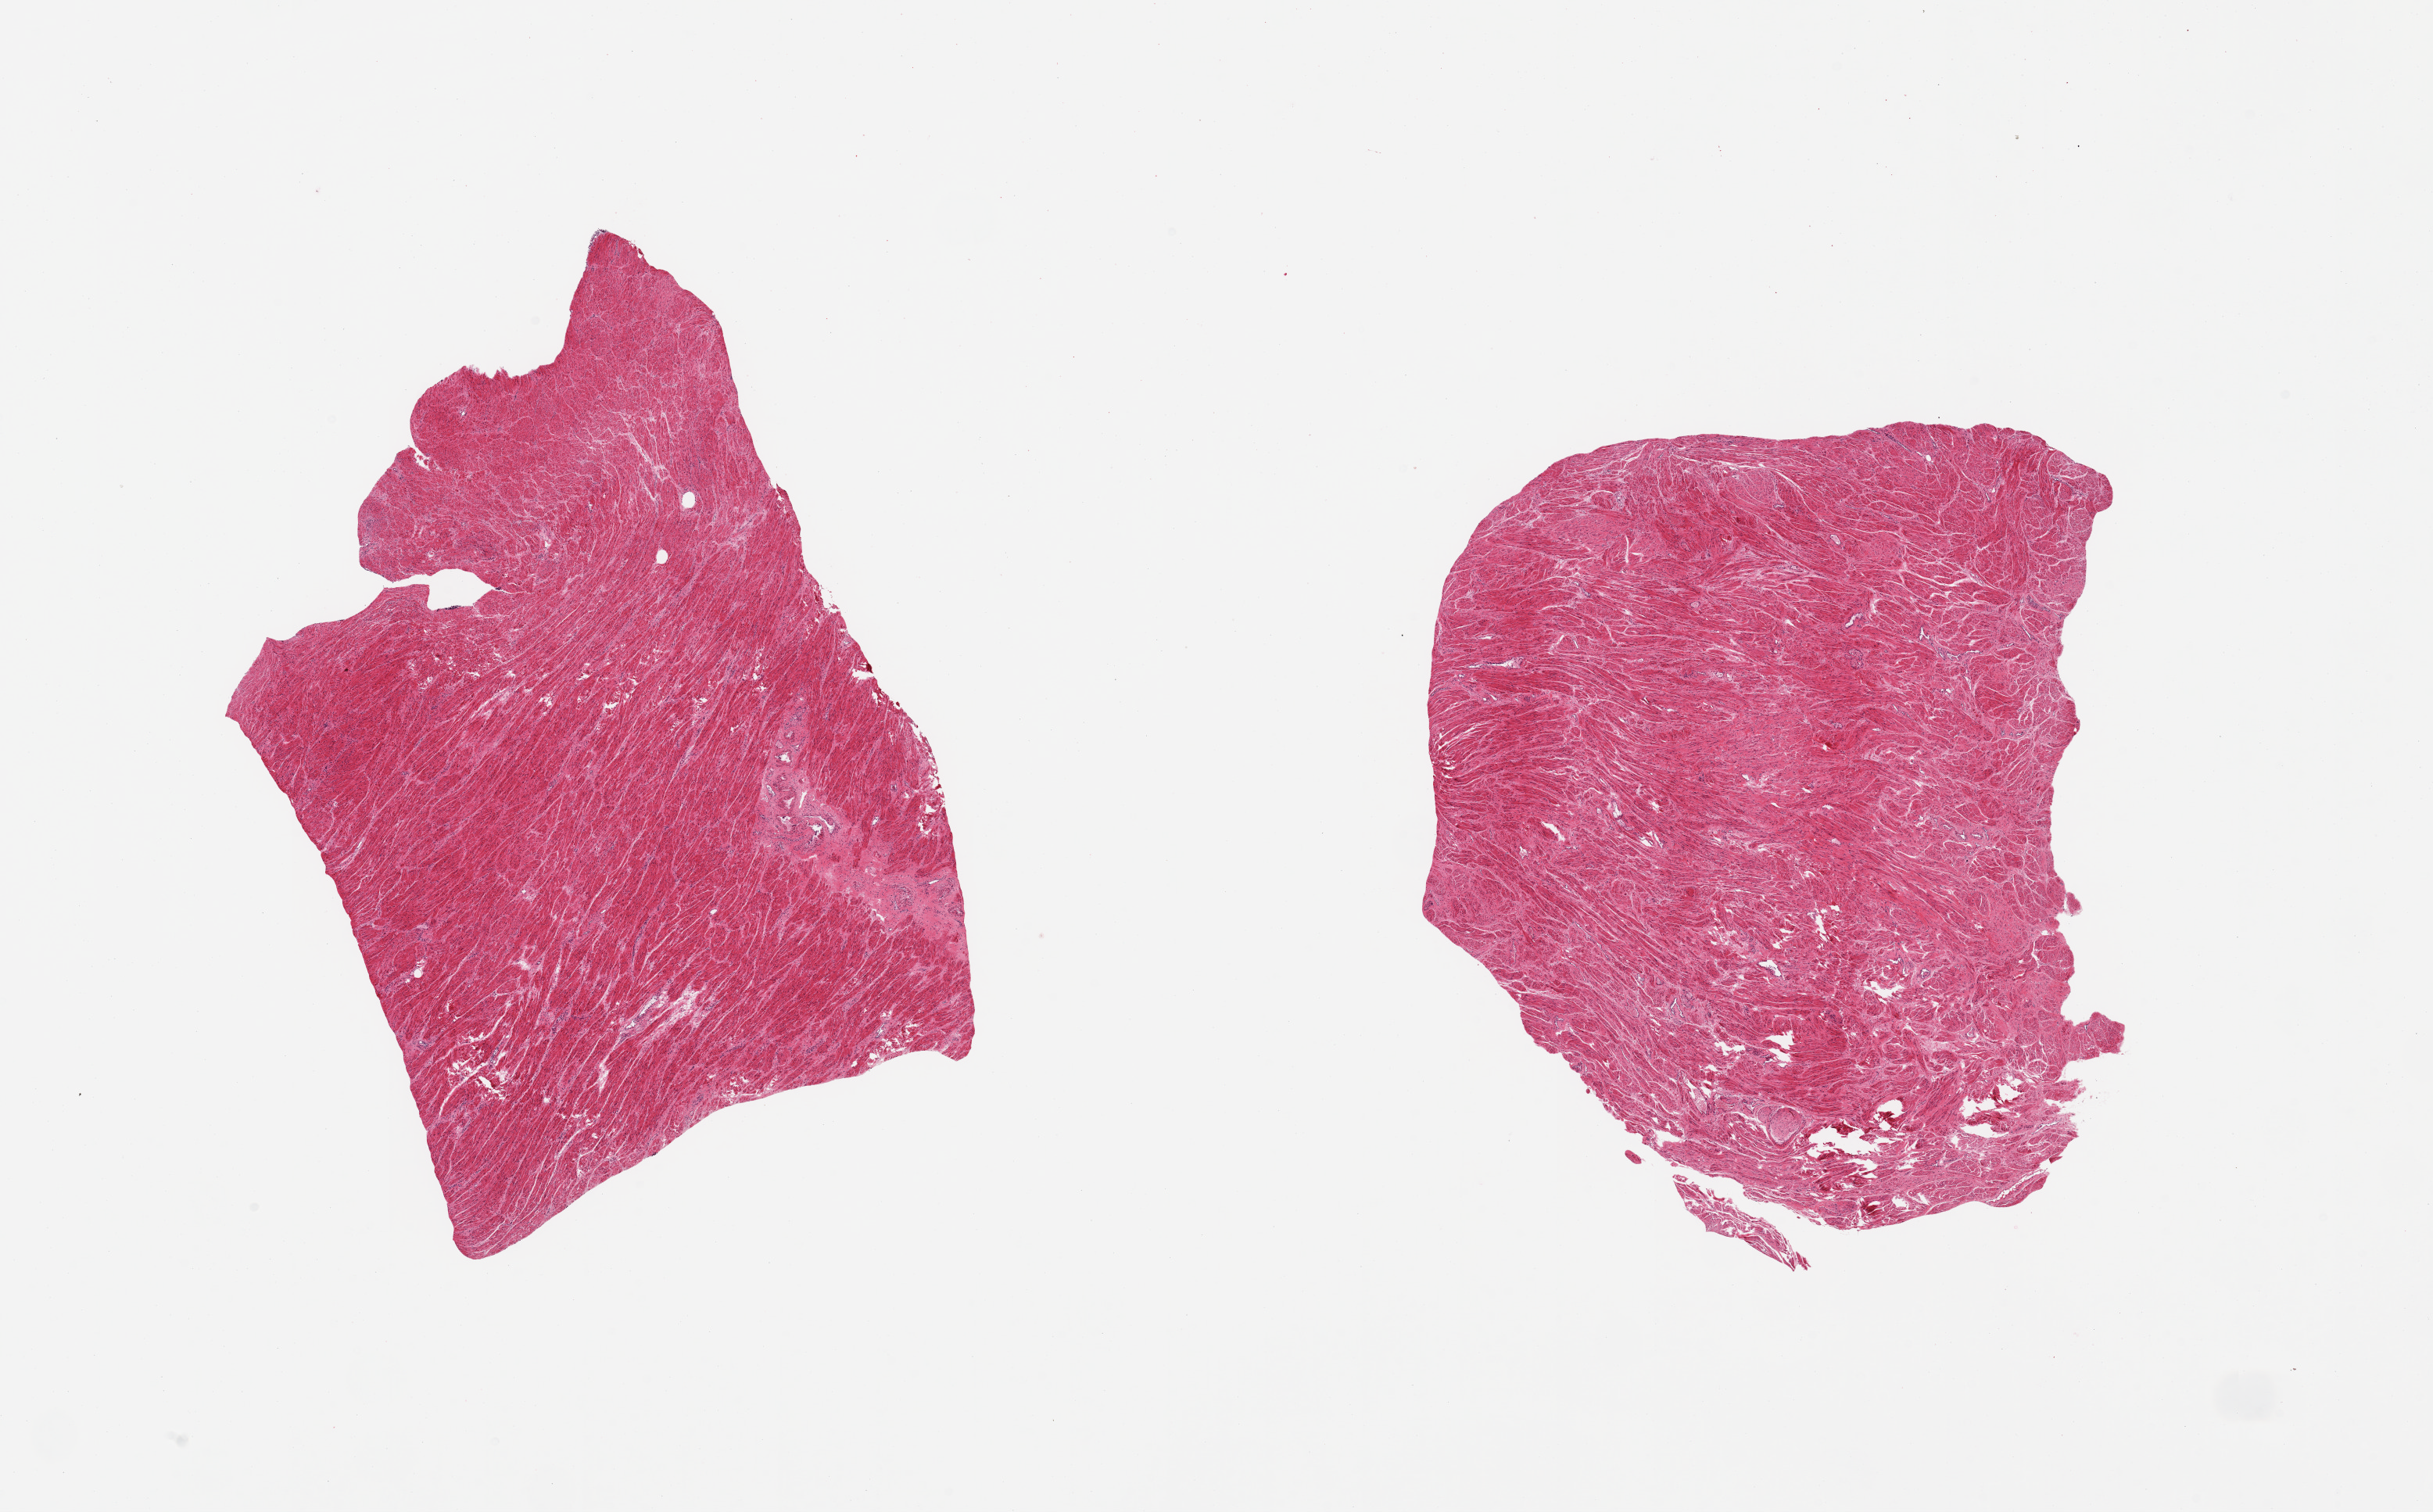
Haematoxylin and eosin whole-slide image — a low-resolution overview of the entire scanned area, about 24.6 x 15.3 mm, PAXgene-fixed, paraffin-embedded tissue, target tissue: prostate, tissue donor sample. Donor: male.
Review note (as recorded): 2 pieces; fibromuscular stroma only.